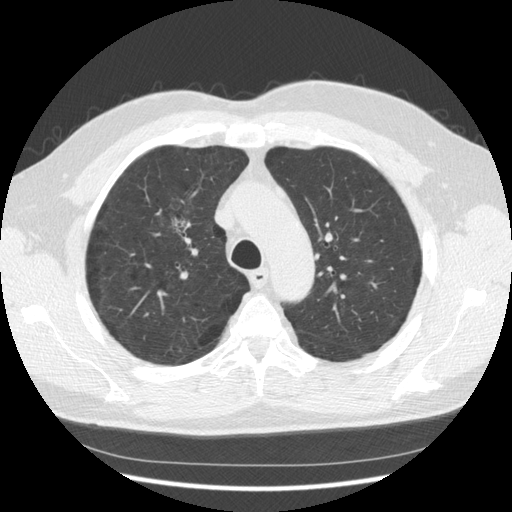
Low-dose screening chest CT, one axial slice. Slice 92 of 133 in the series (ordered by position). 140 kVp. Lung window (W 1500 / L -600 HU). 2.5 mm slice thickness. 512 × 512 image matrix, field of view 369 × 369 mm.
Structures marked on this image (manually delineated by an expert):
- lesion 1 (tumor, upper lobe of right lung): bounding box <172,218,186,233> (left, top, right, bottom; pixels)